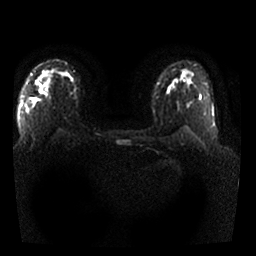
Breast MRI, one axial slice. Slice 19 of 25 in the series (ordered by position). Diffusion-weighted series; image 2 of 4 stored at this slice position (different b-values; order by instance number). 1.5 T. 4 mm slice thickness. 256 × 256 image matrix, field of view 330 × 330 mm. Female patient.
Annotated regions visible in this slice (expert manual segmentation):
- tumour on diffusion-weighted imaging: box from (x=40, y=90) to (x=43, y=92) px